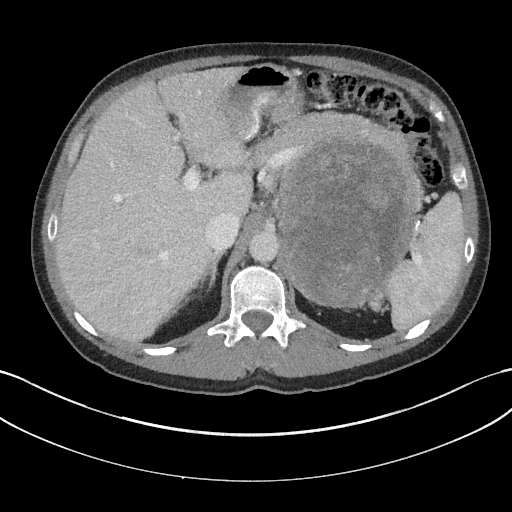
Contrast-enhanced abdominal CT, one axial slice. Position 119 of 147 along the scan axis. Soft-tissue window (W 400 / L 40 HU). 3 mm slice thickness. 512 × 512 image matrix. Male patient, age 58 years. Case-level facts recorded for this patient, not image findings: diagnosis: adrenocortical carcinoma; tumour side: left adrenal; tumour size at pathology: 22 cm; Ki-67 index: 26 %; stage (as recorded): 2.
Outlined on this slice (semi-automatically segmented with operator editing):
- mass: box from (x=282, y=139) to (x=411, y=305) px